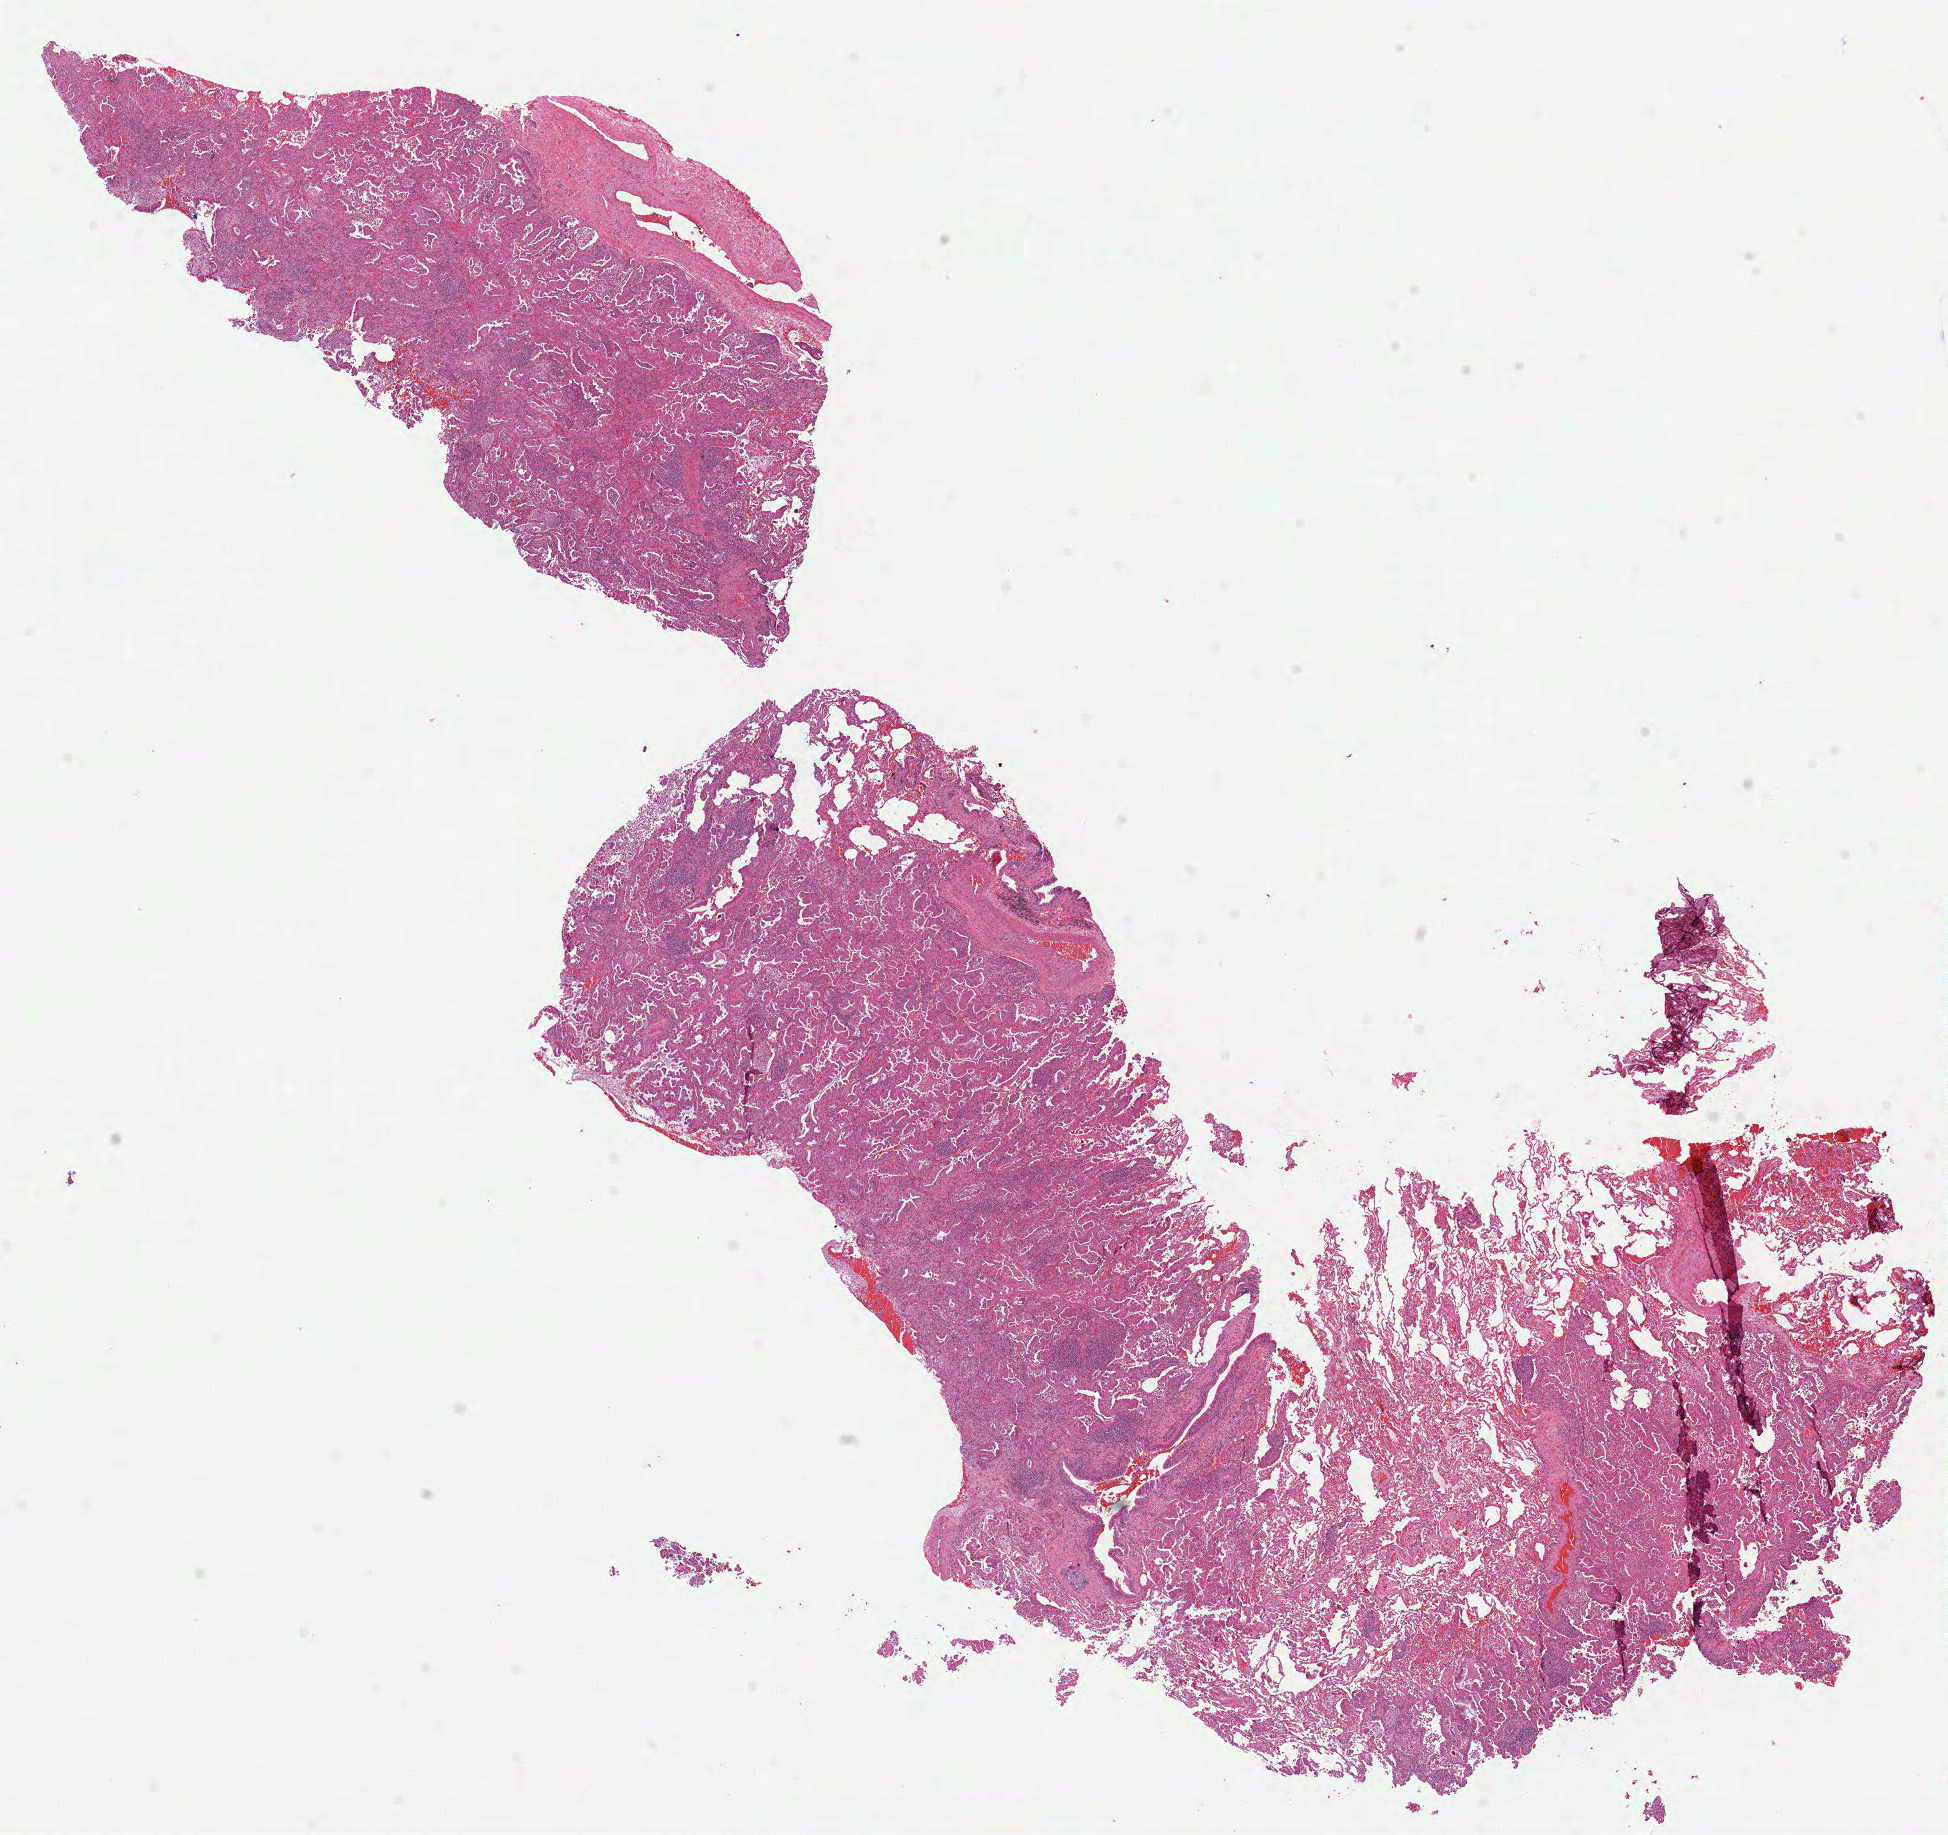
Digitized Hematoxylin and eosin (H&E) stained tissue section (whole slide), a low-resolution overview of the entire scanned area, about 15.7 x 14.8 mm, FFPE section, lung, primary tumour sample. Patient: female, age at initial diagnosis 72 years.
AJCC pathologic stage: IIB. Histologic diagnosis: Mucinous adenocarcinoma (lower lobe, lung).